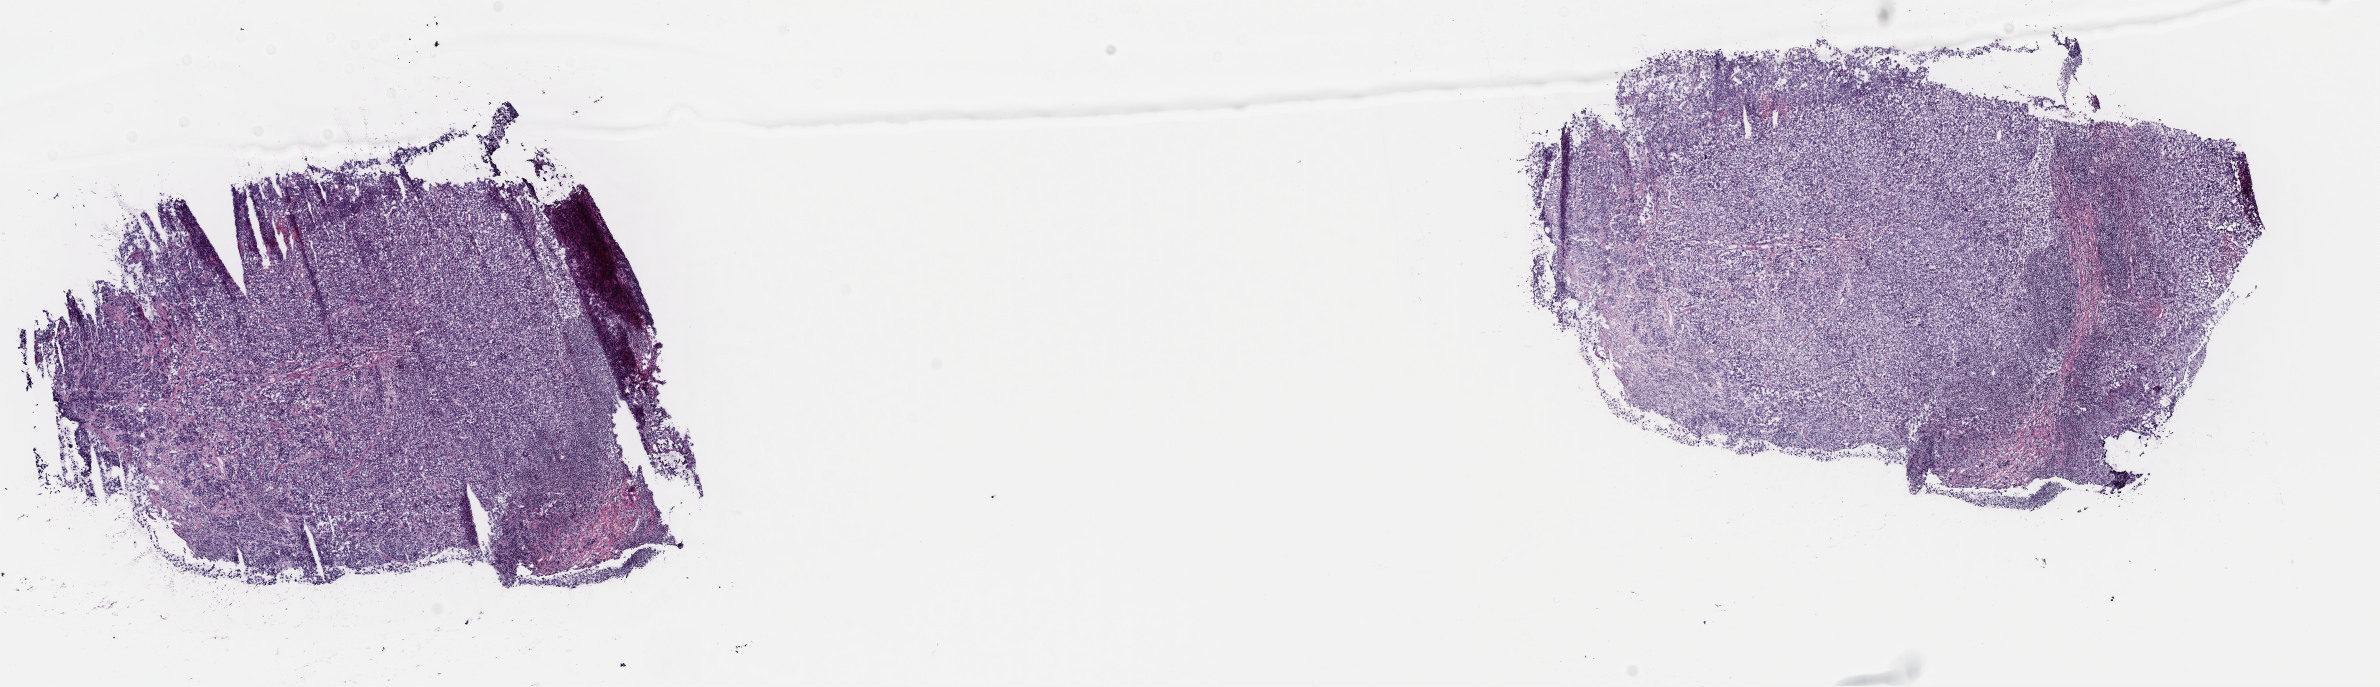
Digitized H&E-stained tissue section (whole slide) — low-resolution overview of the scanned area, about 18.8 x 5.4 mm (acquisition: 40x scan); frozen section; metastatic tumour sample, sampled site: lymph node. Male patient; age at initial diagnosis 62 years. Pathologist review of this section (percent, as recorded): tumour cells 100%, tumour nuclei 90%, normal cells 0%, stromal cells 0%, necrosis 0%. Infiltration values recorded for this section: lymphocyte infiltration 0%, monocyte infiltration 0%, neutrophil infiltration 0%.
This section: metastatic tumour tissue. Patient diagnosis: Malignant melanoma, NOS.